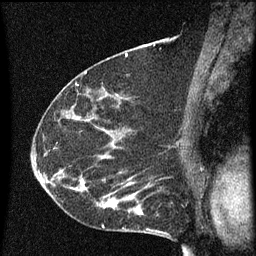
Breast MRI (dynamic contrast-enhanced), one sagittal slice. Position 37 of 60 along the scan axis. Dynamic contrast-enhanced series, image 2 of 3 at this slice position (ordered by acquisition). 1.5 T. TE 4.2 ms, TR 8 ms. 256 × 256 image matrix, field of view 180 × 180 mm. Female patient, age 55 years.
Structures marked on this image (semi-automatically segmented with operator editing):
- analysis volume of interest (the breast-tissue region the enhancement analysis was run in; not a lesion): box from (x=51, y=156) to (x=145, y=217) px
- tumour enhancement mask (voxels above the 70 % enhancement threshold inside the analysis volume of interest): (x=51, y=156)–(x=142, y=215)